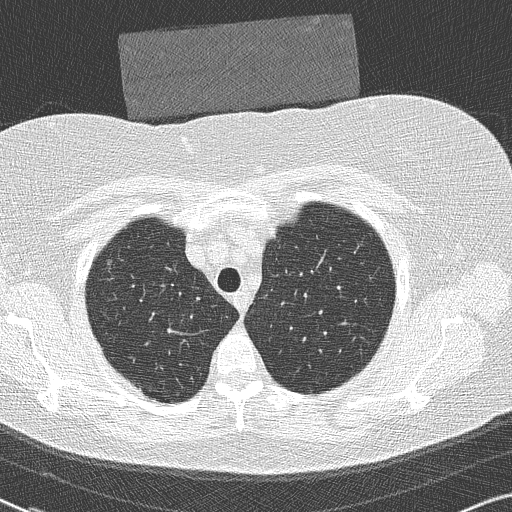
Low-dose screening chest CT, axial slice, first (baseline) screen, lung window (W 1500 / L -600 HU), 2 mm slice thickness, slice 44 of 306 in the series, 512 × 512 image matrix. Female, age 58 years at enrolment.
Expert-annotated lung lesion, bounding box <88,242,132,290> (left, top, right, bottom; pixels). No non-calcified nodule or mass ≥4 mm was recorded by the screening reader at this exam.